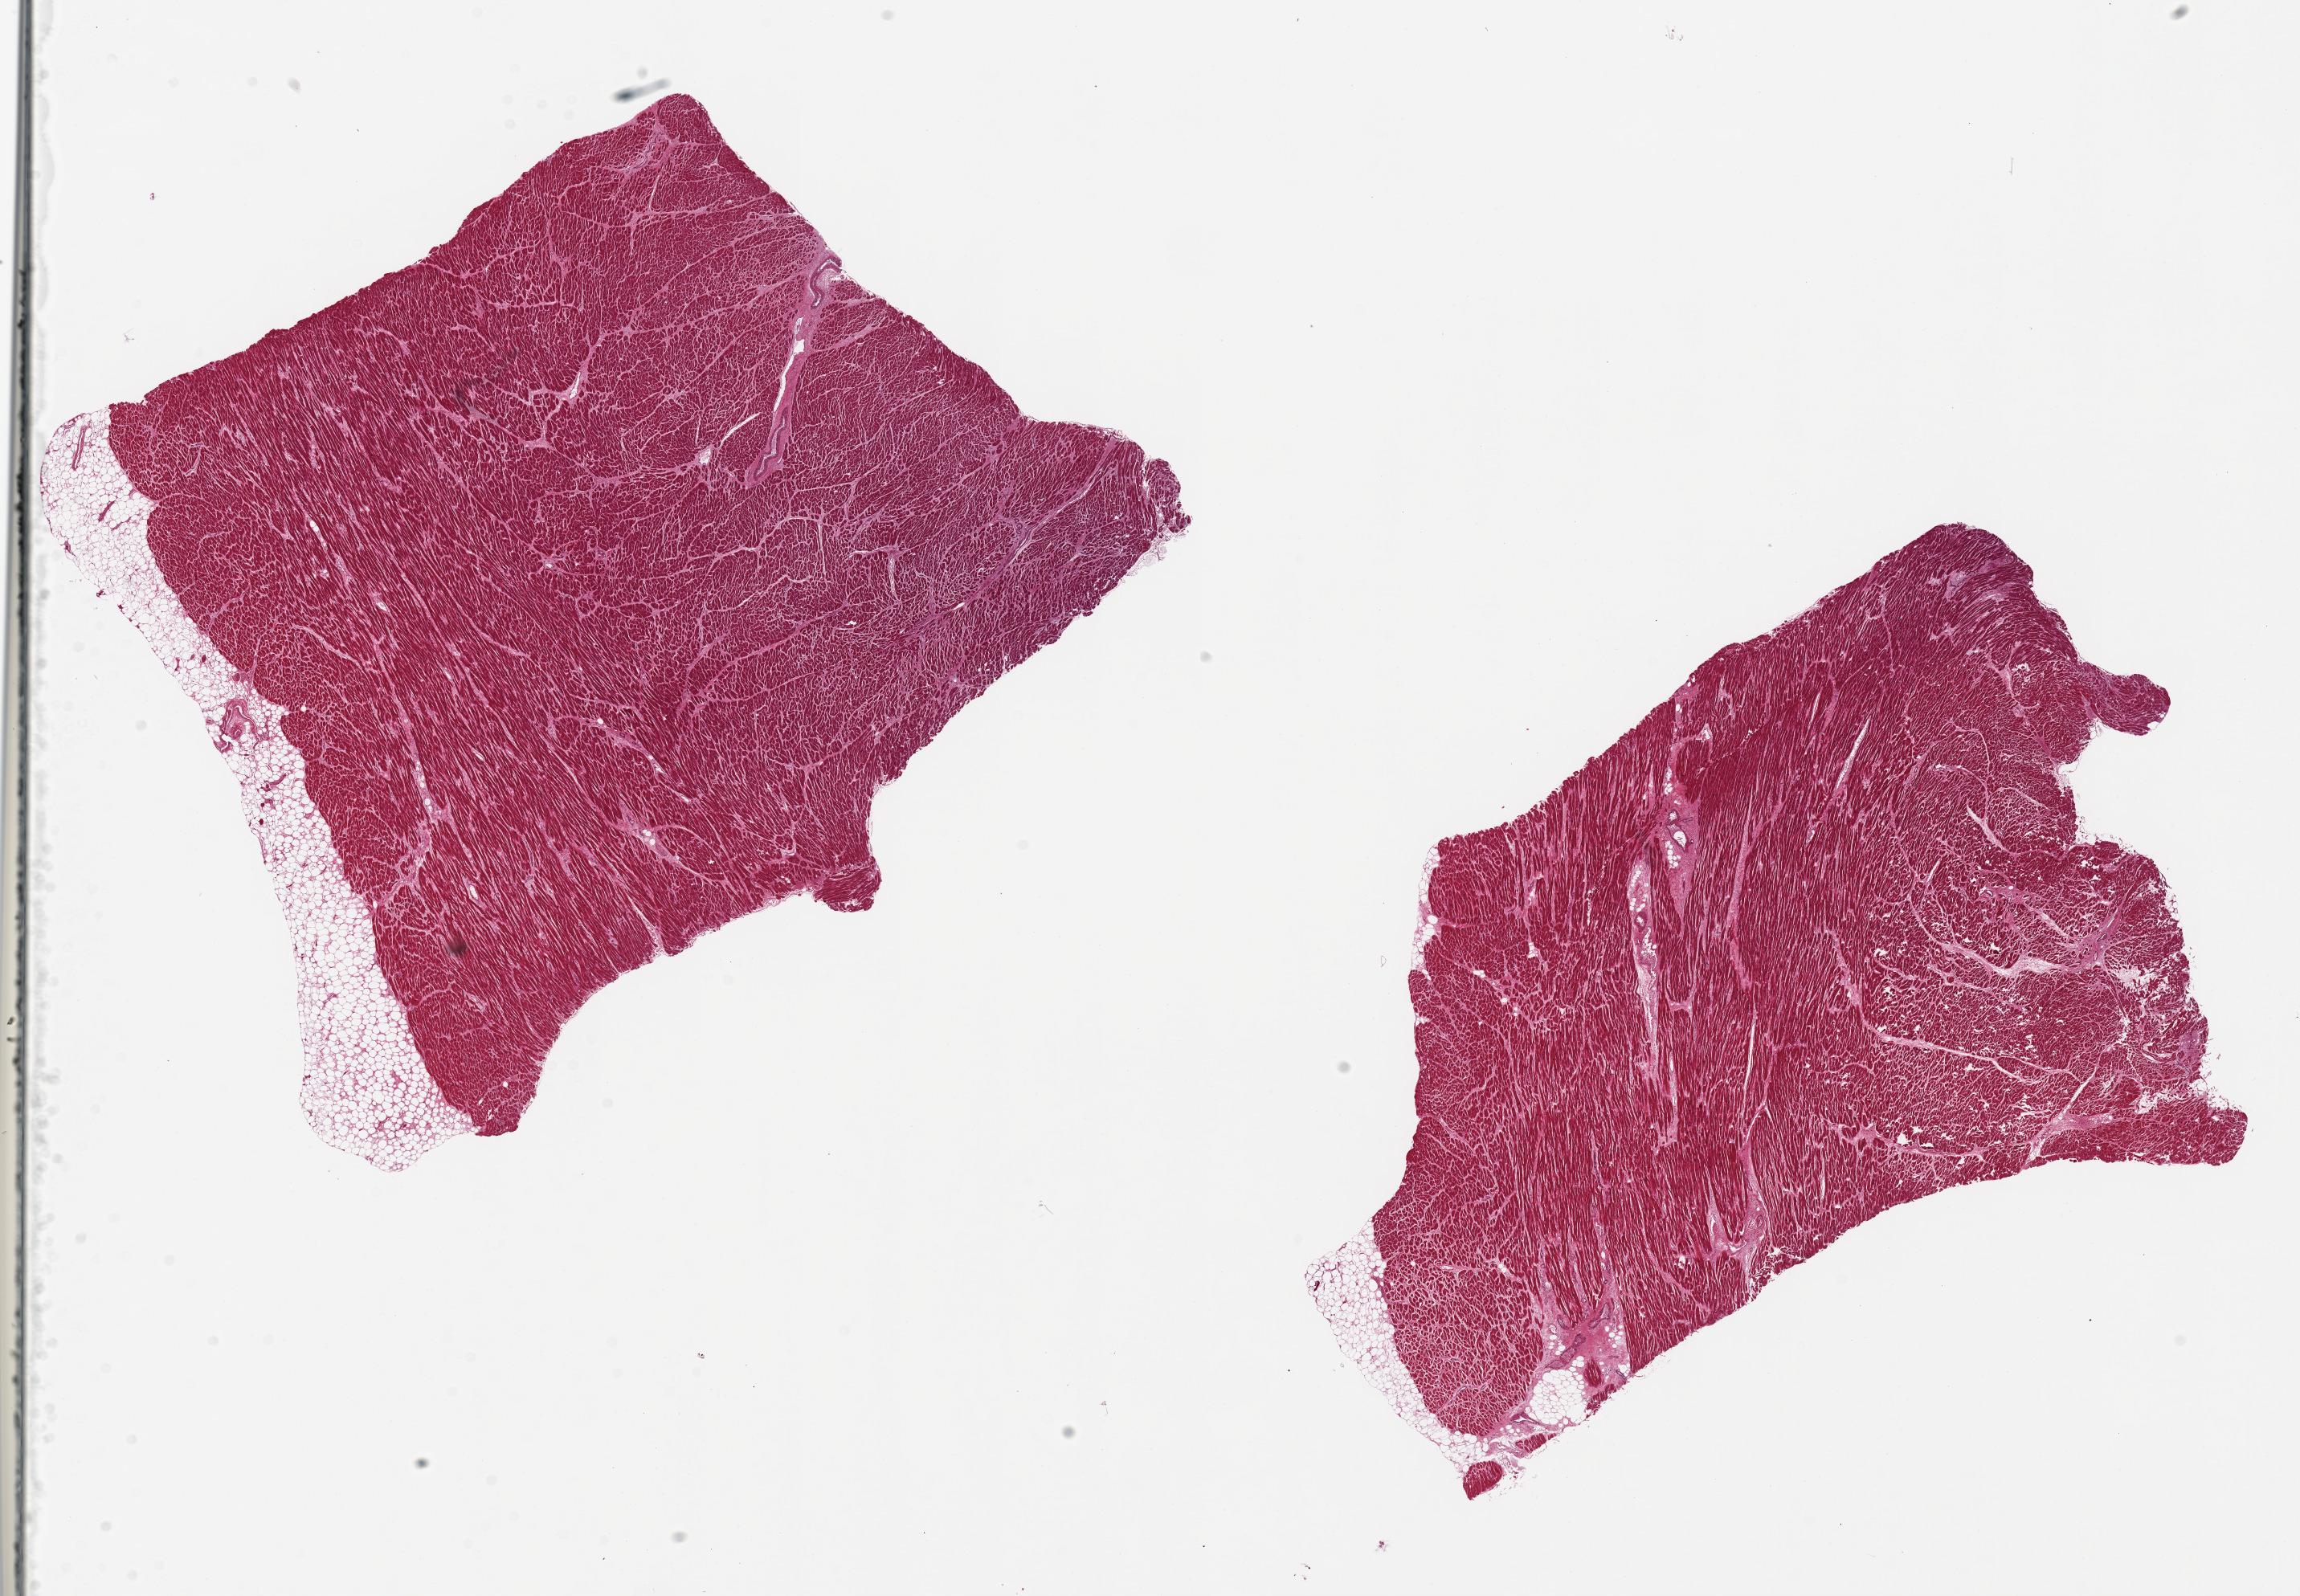
Hematoxylin and eosin (H&E) whole-slide image, whole scanned area (about 22.6 x 15.7 mm, acquisition: 20x scan) shown as a low-resolution overview, PAXgene-fixed, paraffin-embedded tissue, sampled site (target tissue): heart, tissue donor sample. Donor: male.
• review note (as recorded): 2 pieces, moderate interstitial fibrosis/chronic ischemic changes, unusally advance autolysis